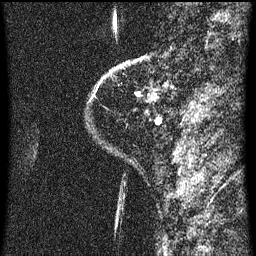
Breast MRI (dynamic contrast-enhanced), one sagittal slice. Position 6 of 60 along the scan axis. Dynamic contrast-enhanced series, image 2 of 3 at this slice position (ordered by acquisition). 1.5 T. TE 4.2 ms, TR 8 ms. 2 mm slice thickness. 256 × 256 image matrix, field of view 180 × 180 mm. Patient: female, 48 years.
Annotated regions visible in this slice (semi-automatic segmentation, software-assisted and operator-edited):
- analysis volume of interest (the breast-tissue region the enhancement analysis was run in; not a lesion): box from (x=128, y=54) to (x=173, y=125) px
- tumour enhancement mask (voxels above the 70 % enhancement threshold inside the analysis volume of interest): (x=136, y=92)–(x=161, y=125)